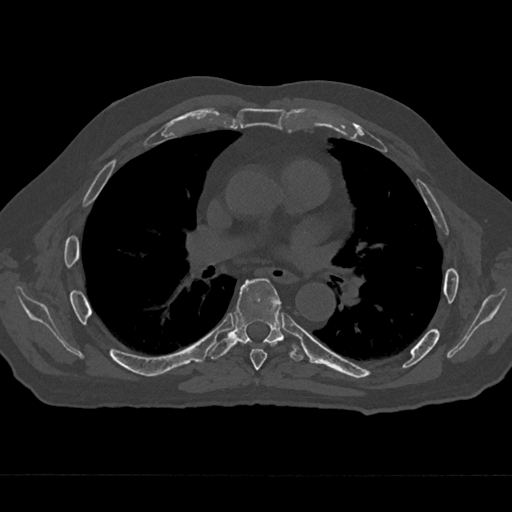
CT including the spine, one axial slice; position 394 of 797 along the scan axis; reconstruction kernel Br40s/3; 120 kVp; bone window (W 1800 / L 400 HU); 512 × 512 image matrix. Male patient, age 75 years. Case-level facts recorded for this patient, not image findings: primary cancer: renal.
Structures marked on this image (semi-automatically segmented with operator editing):
- T6 vertebra: box from (x=241, y=342) to (x=277, y=371) px
- T7 vertebra: (x=208, y=278)–(x=304, y=361)